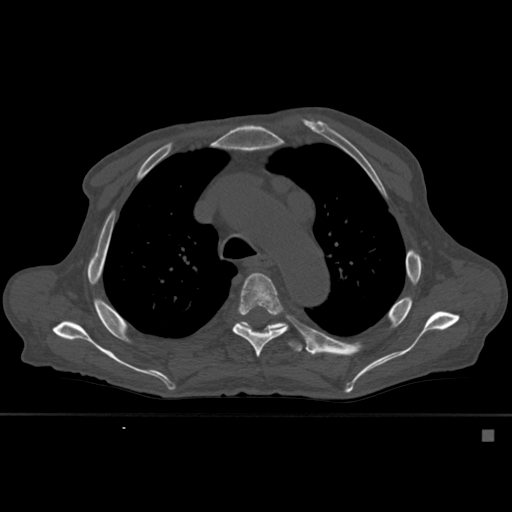
CT including the spine, one axial slice; position 400 of 527 along the scan axis; bone window (W 1800 / L 400 HU); 1.5 mm slice thickness; 512 × 512 image matrix, field of view 373 × 373 mm. Male patient, age 78 years. Case-level facts recorded for this patient, not image findings: primary cancer: prostate.
Annotated regions visible in this slice (semi-automatic segmentation, software-assisted and operator-edited):
- T5 vertebra: bounding box (x1, y1, x2, y2) in pixels: (232, 273, 289, 358)
- T6 vertebra: (243, 323, 303, 353)